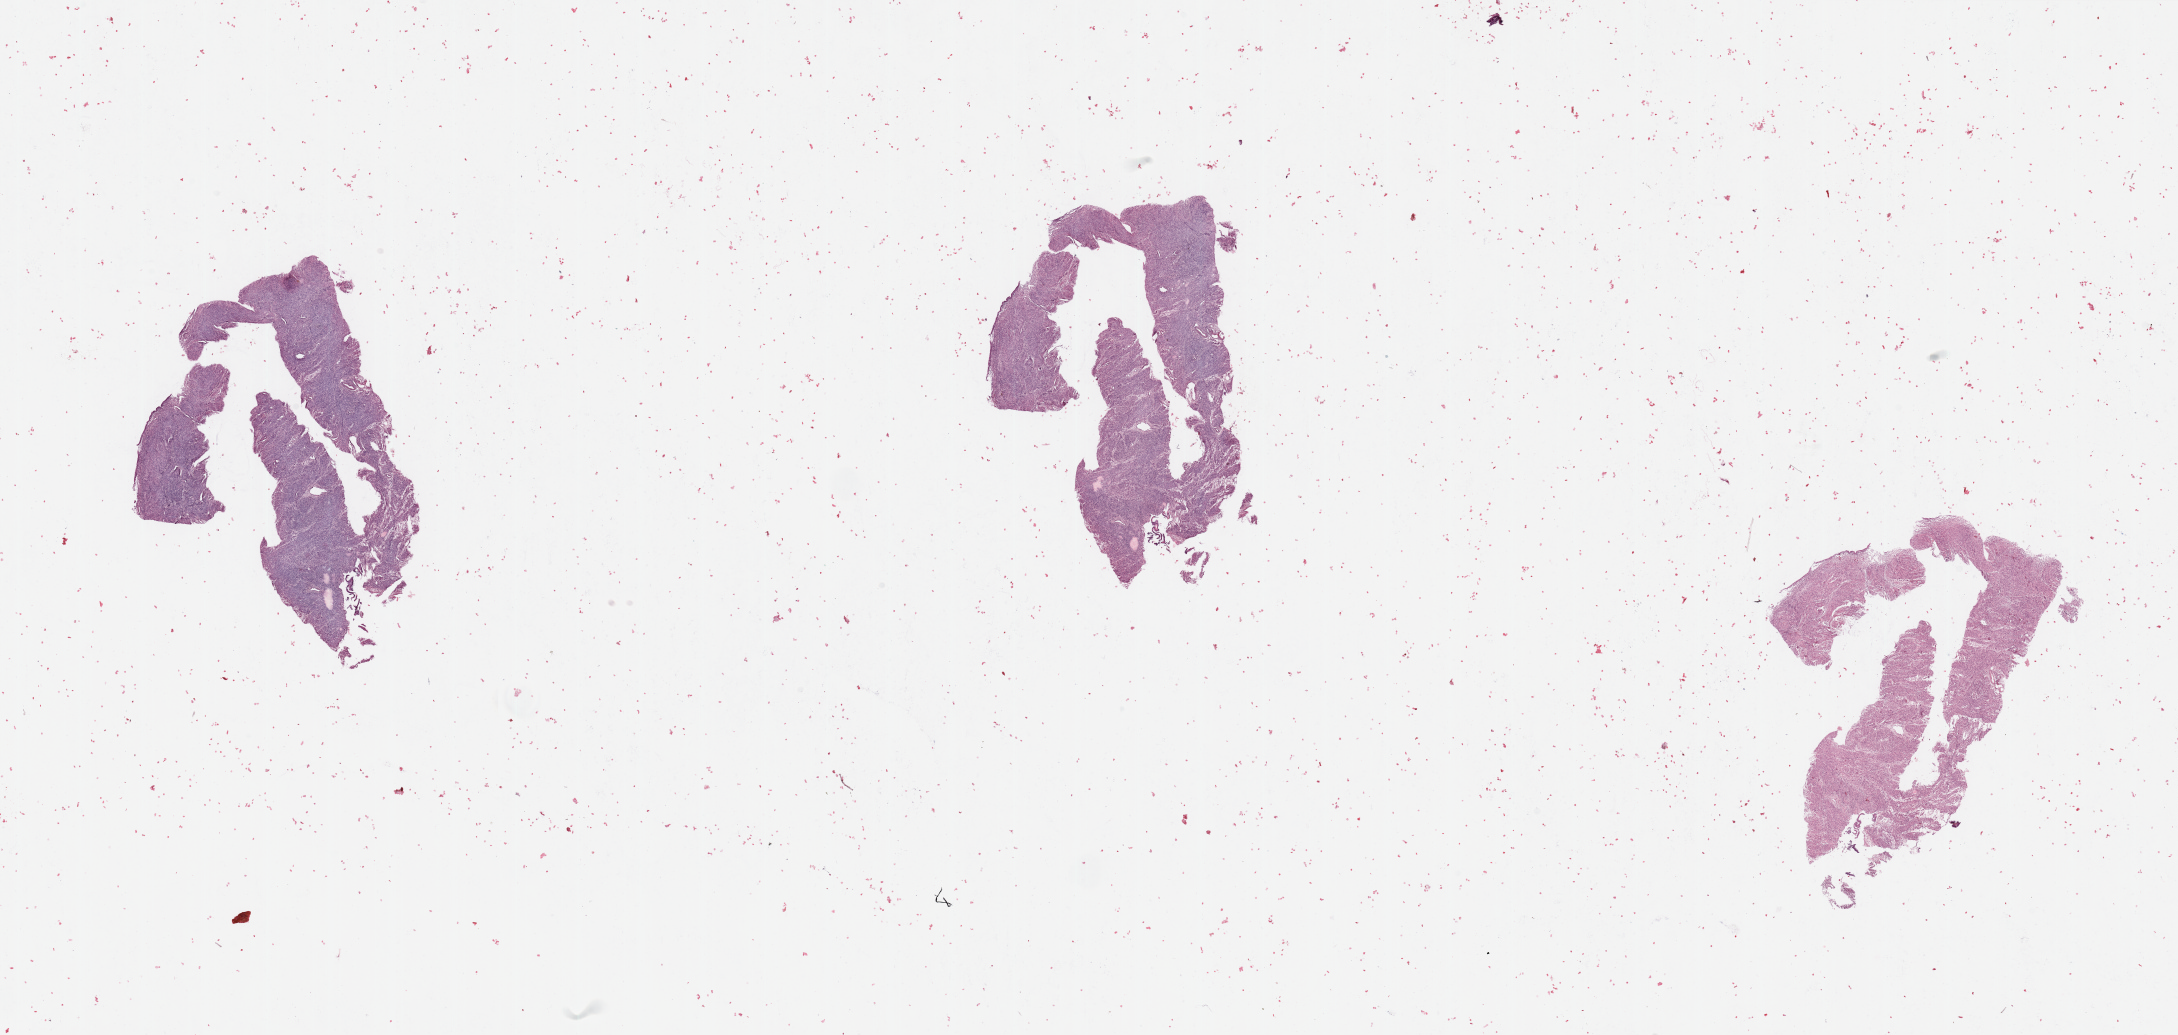
Whole-slide histology image, H&E, whole scanned area (about 34.5 x 16.4 mm) shown as a low-resolution overview. Uterus, normal (non-tumour) tissue. Female, 72 y/o.
* this section: normal (non-tumour) tissue from the same patient
* patient diagnosis: Endometrioid adenocarcinoma, NOS